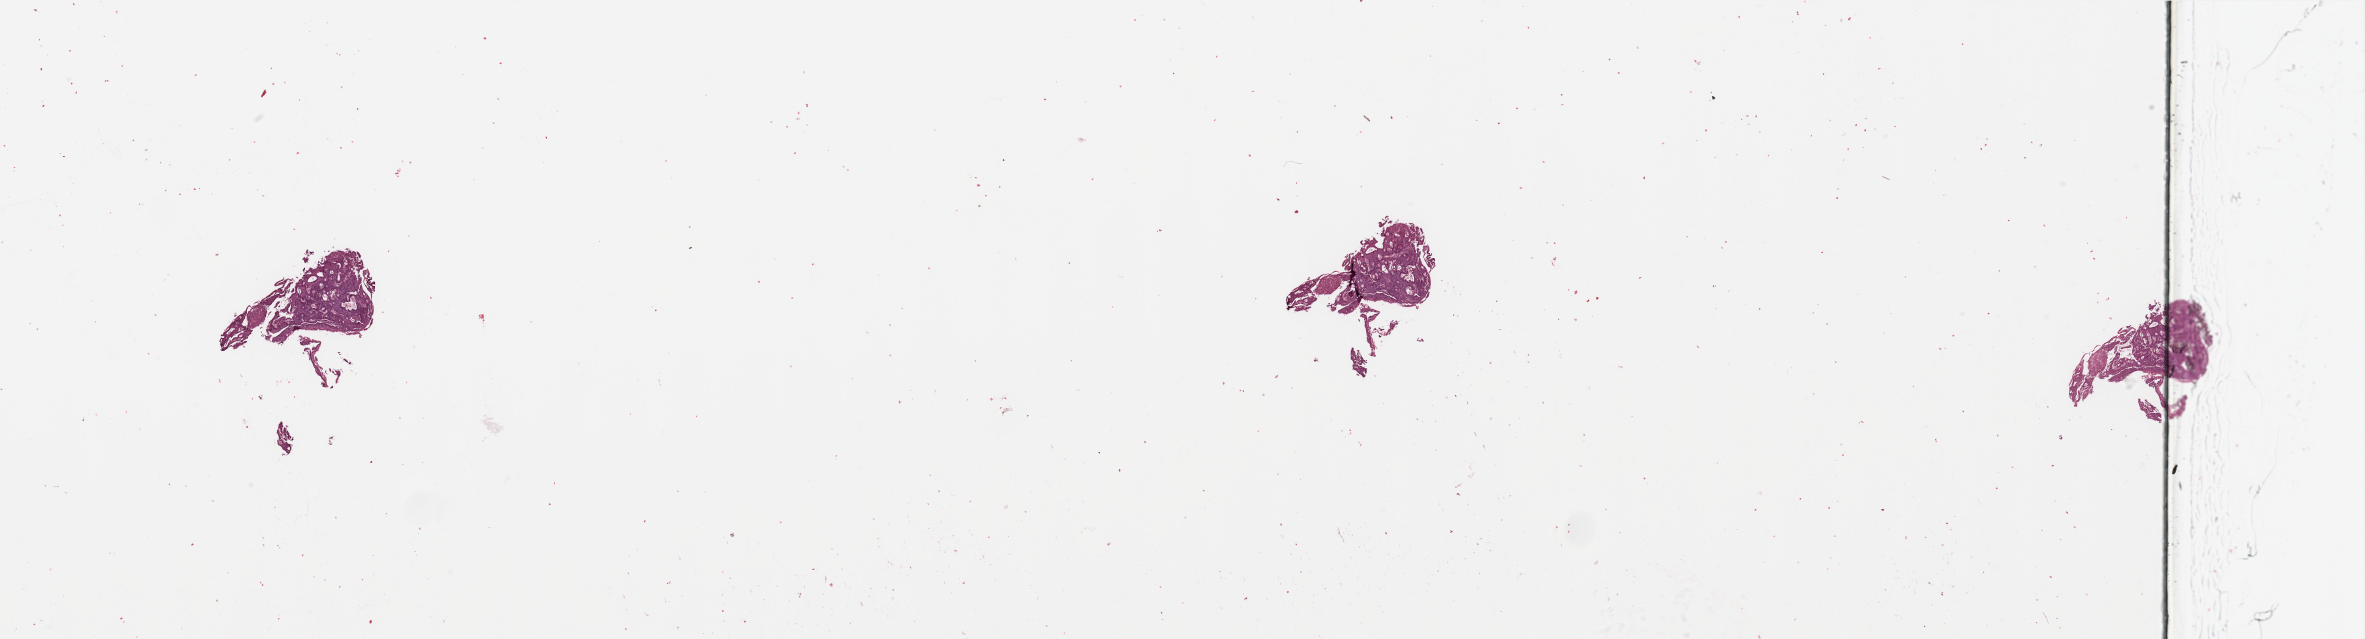
H&E-stained whole-slide image, low-resolution overview of the scanned area, about 37.4 x 10.1 mm, tumour tissue sample, sampled site: uterus. Female, 68 y/o. Histologic grade: G2 (moderately differentiated). Composition of this section per pathologist review: tumour nuclei 90%, necrosis 3%.
* primary tumour site (as recorded): anterior endometrium
* histologic diagnosis: Endometrioid adenocarcinoma, NOS
* AJCC pathologic stage: I